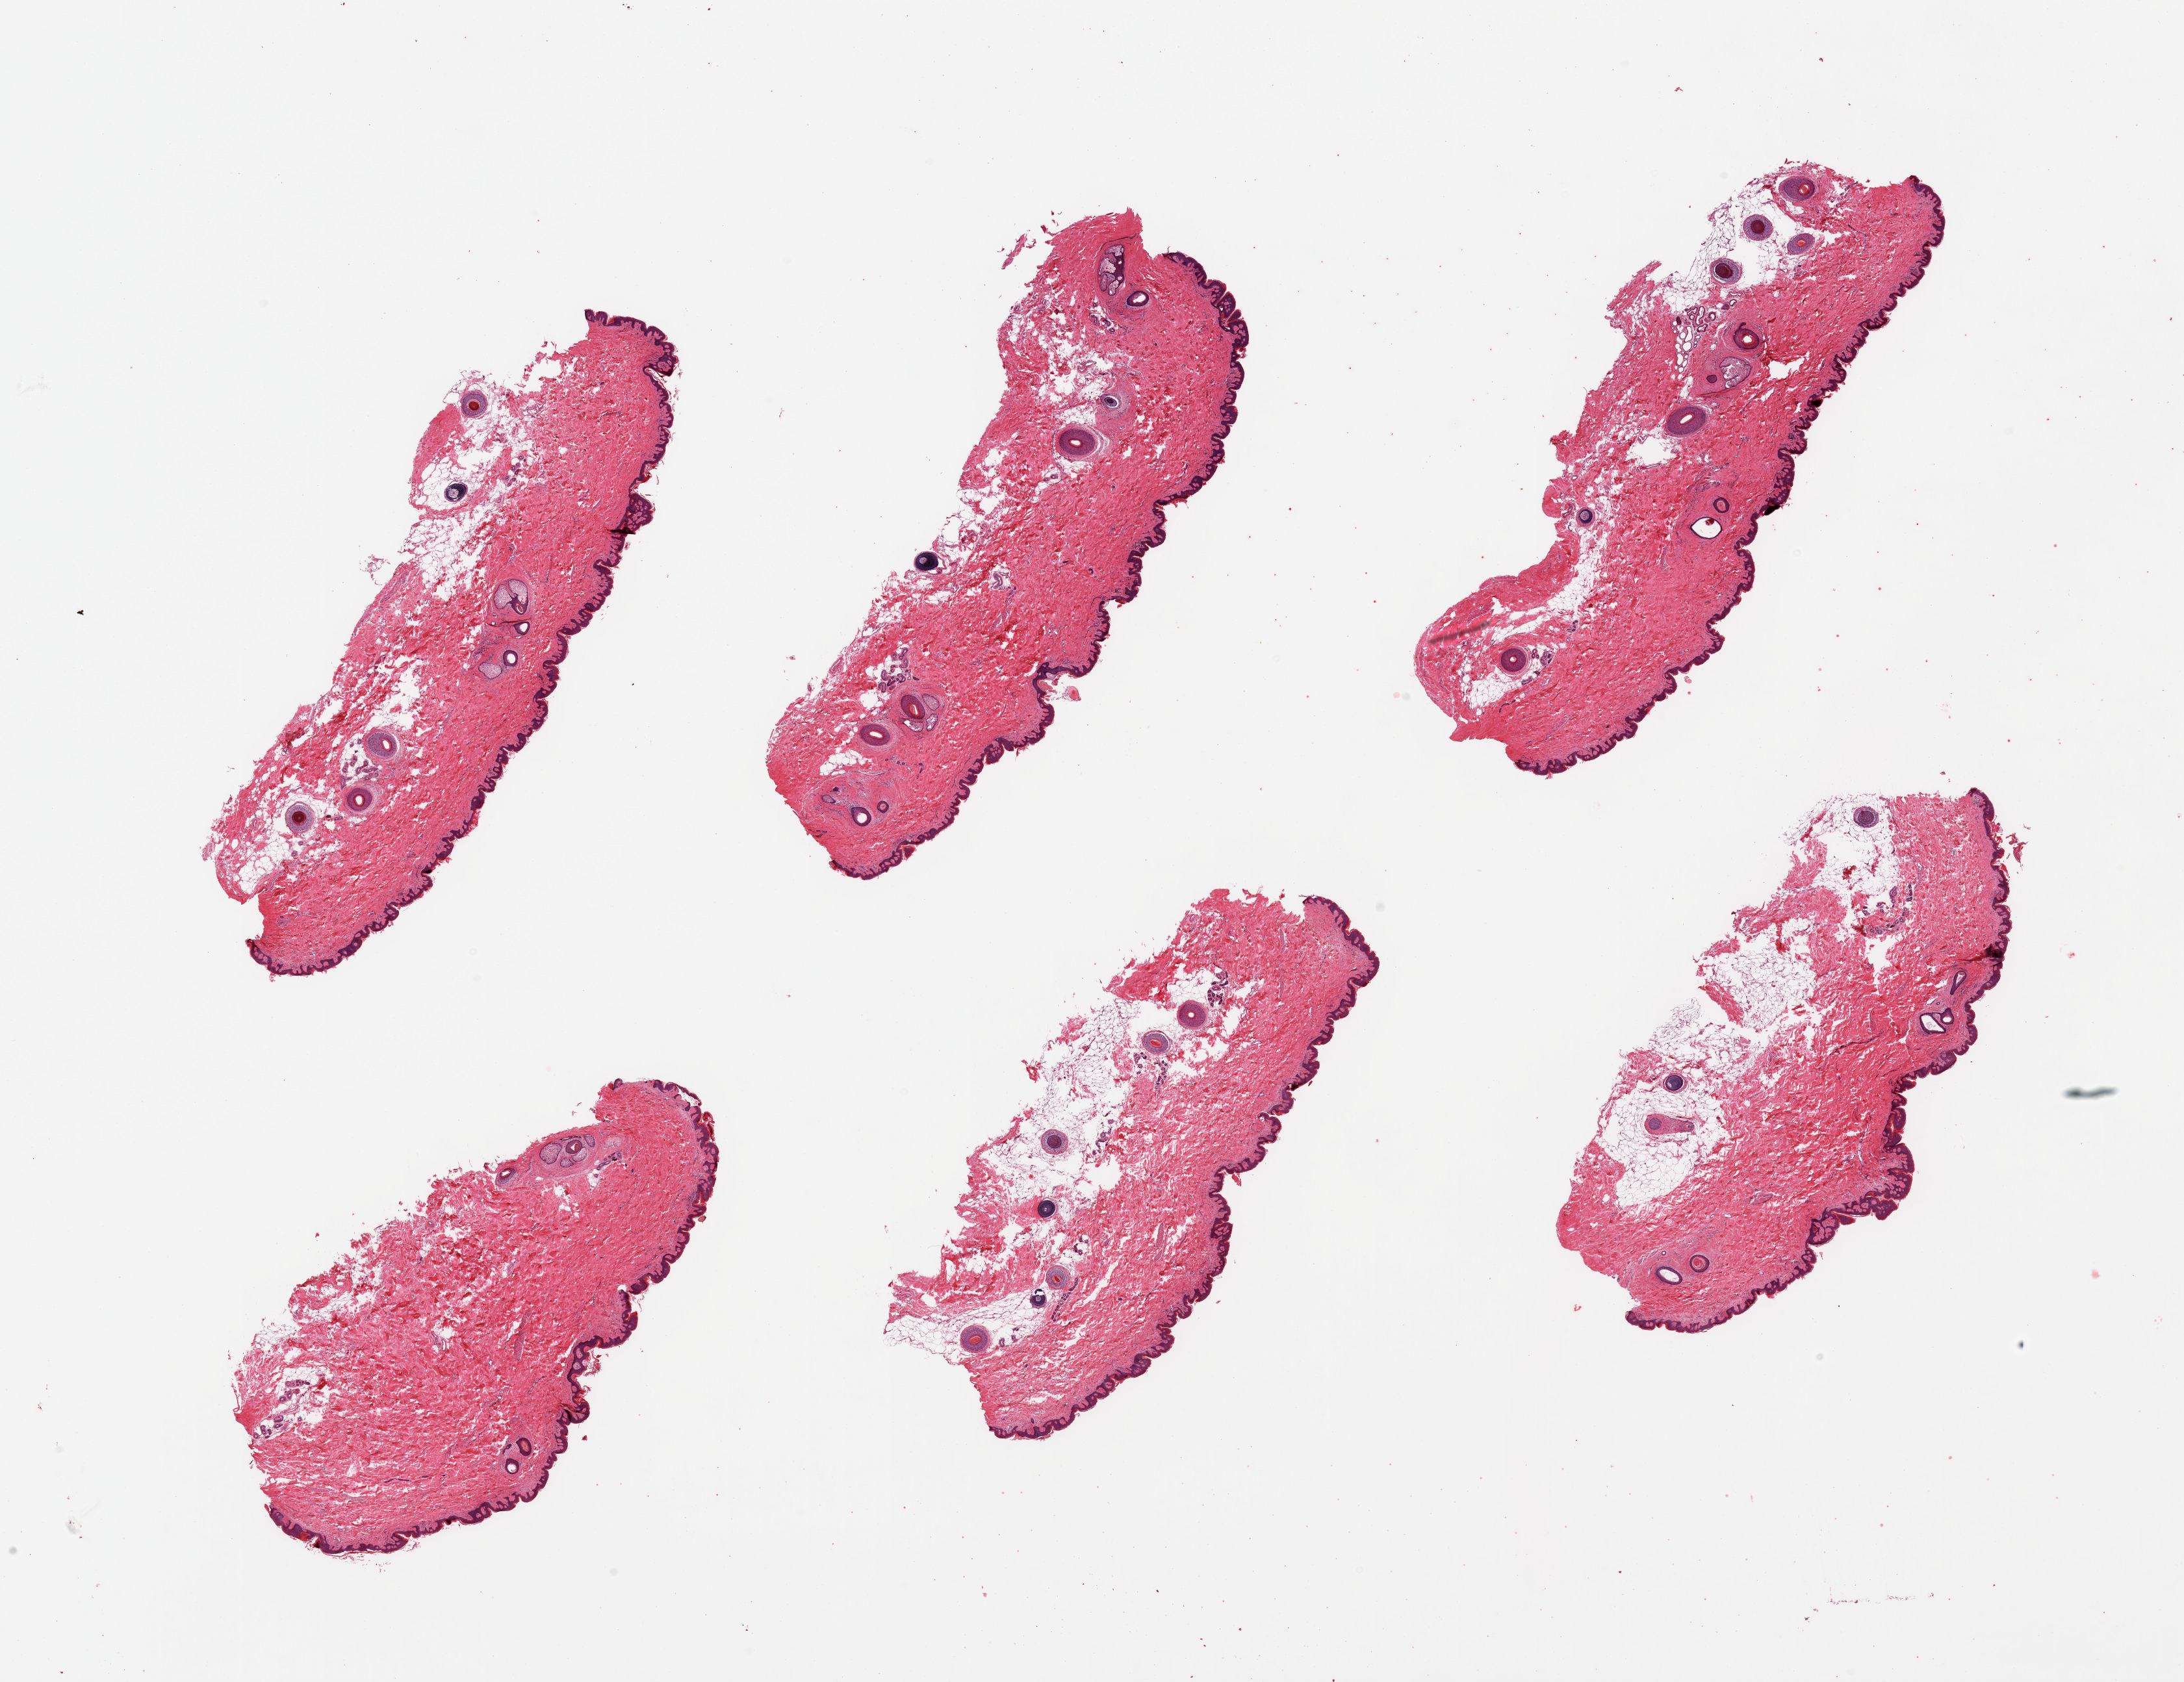
Haematoxylin and eosin whole-slide image, shown as a low-resolution overview of the whole scanned area (about 26.6 x 20.5 mm); PAXgene-fixed paraffin-embedded (PFPE) section; target tissue: skin of suprapubic region; donor tissue sample. Male donor.
Review note (as recorded): 6 pieces; hair bearing skin with ~10 to 20% internal/external fat.